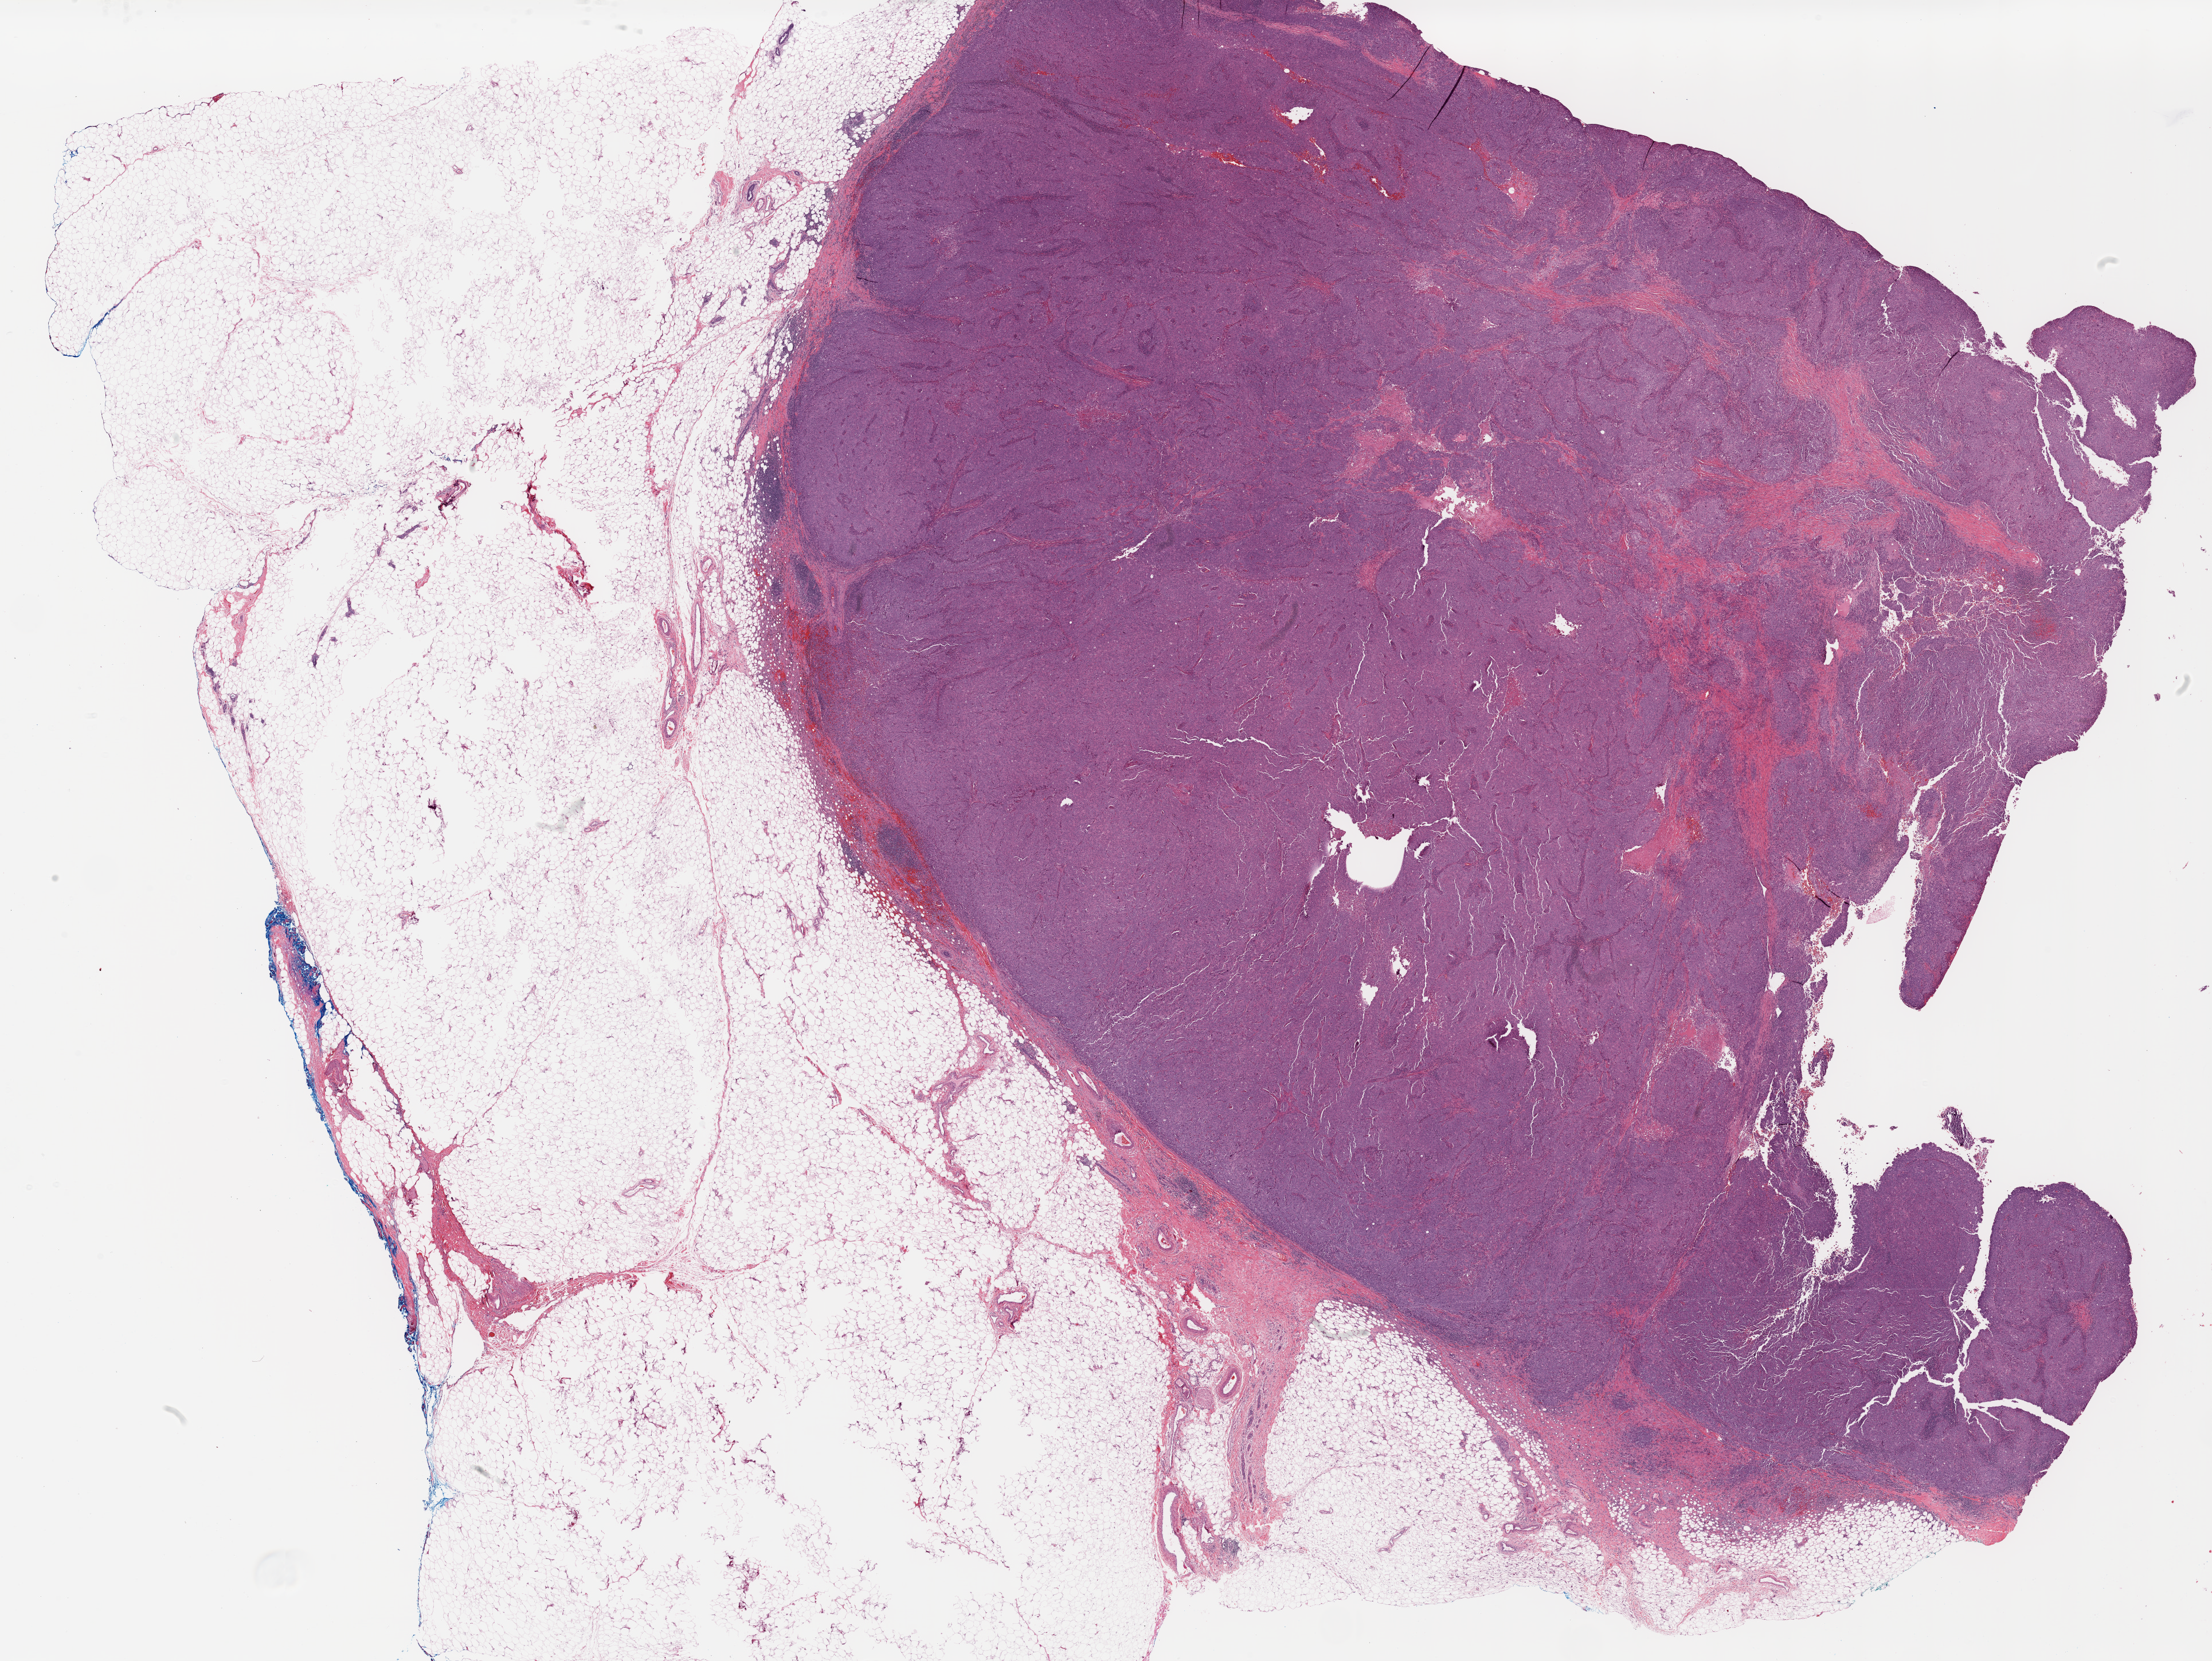
Digitized H&E-stained tissue section (whole slide), low-resolution overview of the scanned area, about 30.8 x 23.1 mm, formalin-fixed paraffin-embedded (FFPE) diagnostic section, breast, primary tumour sample. Patient: female, age at initial diagnosis 61 years.
TNM: T2 N0 (i-) M0. Laterality: left. AJCC pathologic stage: IIA. Histologic diagnosis: Infiltrating duct carcinoma, NOS. Lymph nodes positive (case pathology): 0 of 4 examined.